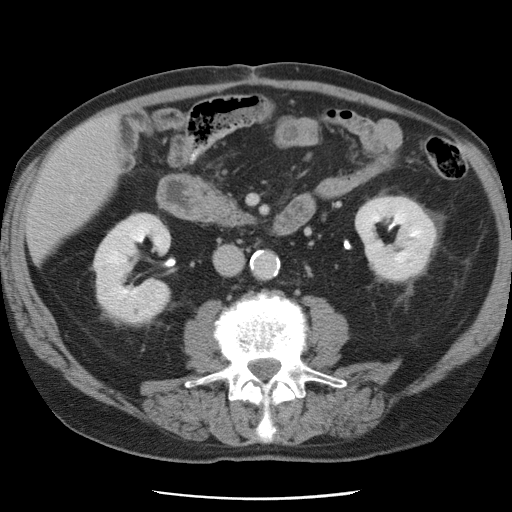
Contrast-enhanced abdominal CT, one axial slice. Slice 21 of 78 in the series (ordered by position). 120 kVp. Intravenous contrast given. Soft-tissue window (W 400 / L 40 HU). 5 mm slice thickness. 512 × 512 image matrix, field of view 337 × 337 mm. Male patient, age 75 years. Case-level facts recorded for this patient, not image findings: diagnosis: colorectal cancer liver metastases, imaged before liver resection; multiple liver metastases: yes; largest metastasis: 2.4 cm; disease in both lobes: yes.
Structures marked on this image (outlined manually by an expert reader):
- liver: bounding box <28,117,117,260> (left, top, right, bottom; pixels)
- planned liver remnant (the part of the liver to remain after resection): <27,120,116,259>